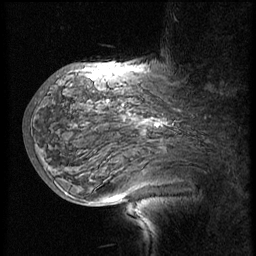
Breast MRI (dynamic contrast-enhanced), one sagittal slice. Position 40 of 60 along the scan axis. 3 images stored at this slice position (order not interpretable as contrast timing). 1.5 T. TE 4.2 ms, TR 8.9 ms. 2.5 mm slice thickness. 256 × 256 image matrix. Female patient, age 57 years. Case-level facts recorded for this patient, not image findings: setting: breast cancer imaged before/during neoadjuvant chemotherapy; receptor status: HER2-positive.
Outlined on this slice (semi-automatically segmented with operator editing):
- analysis volume of interest (the breast-tissue region the enhancement analysis was run in; not a lesion): bounding box <34,75,214,171> (left, top, right, bottom; pixels)
- tumour enhancement mask (voxels above the 140 % enhancement threshold inside the analysis volume of interest): <107,100,162,127>